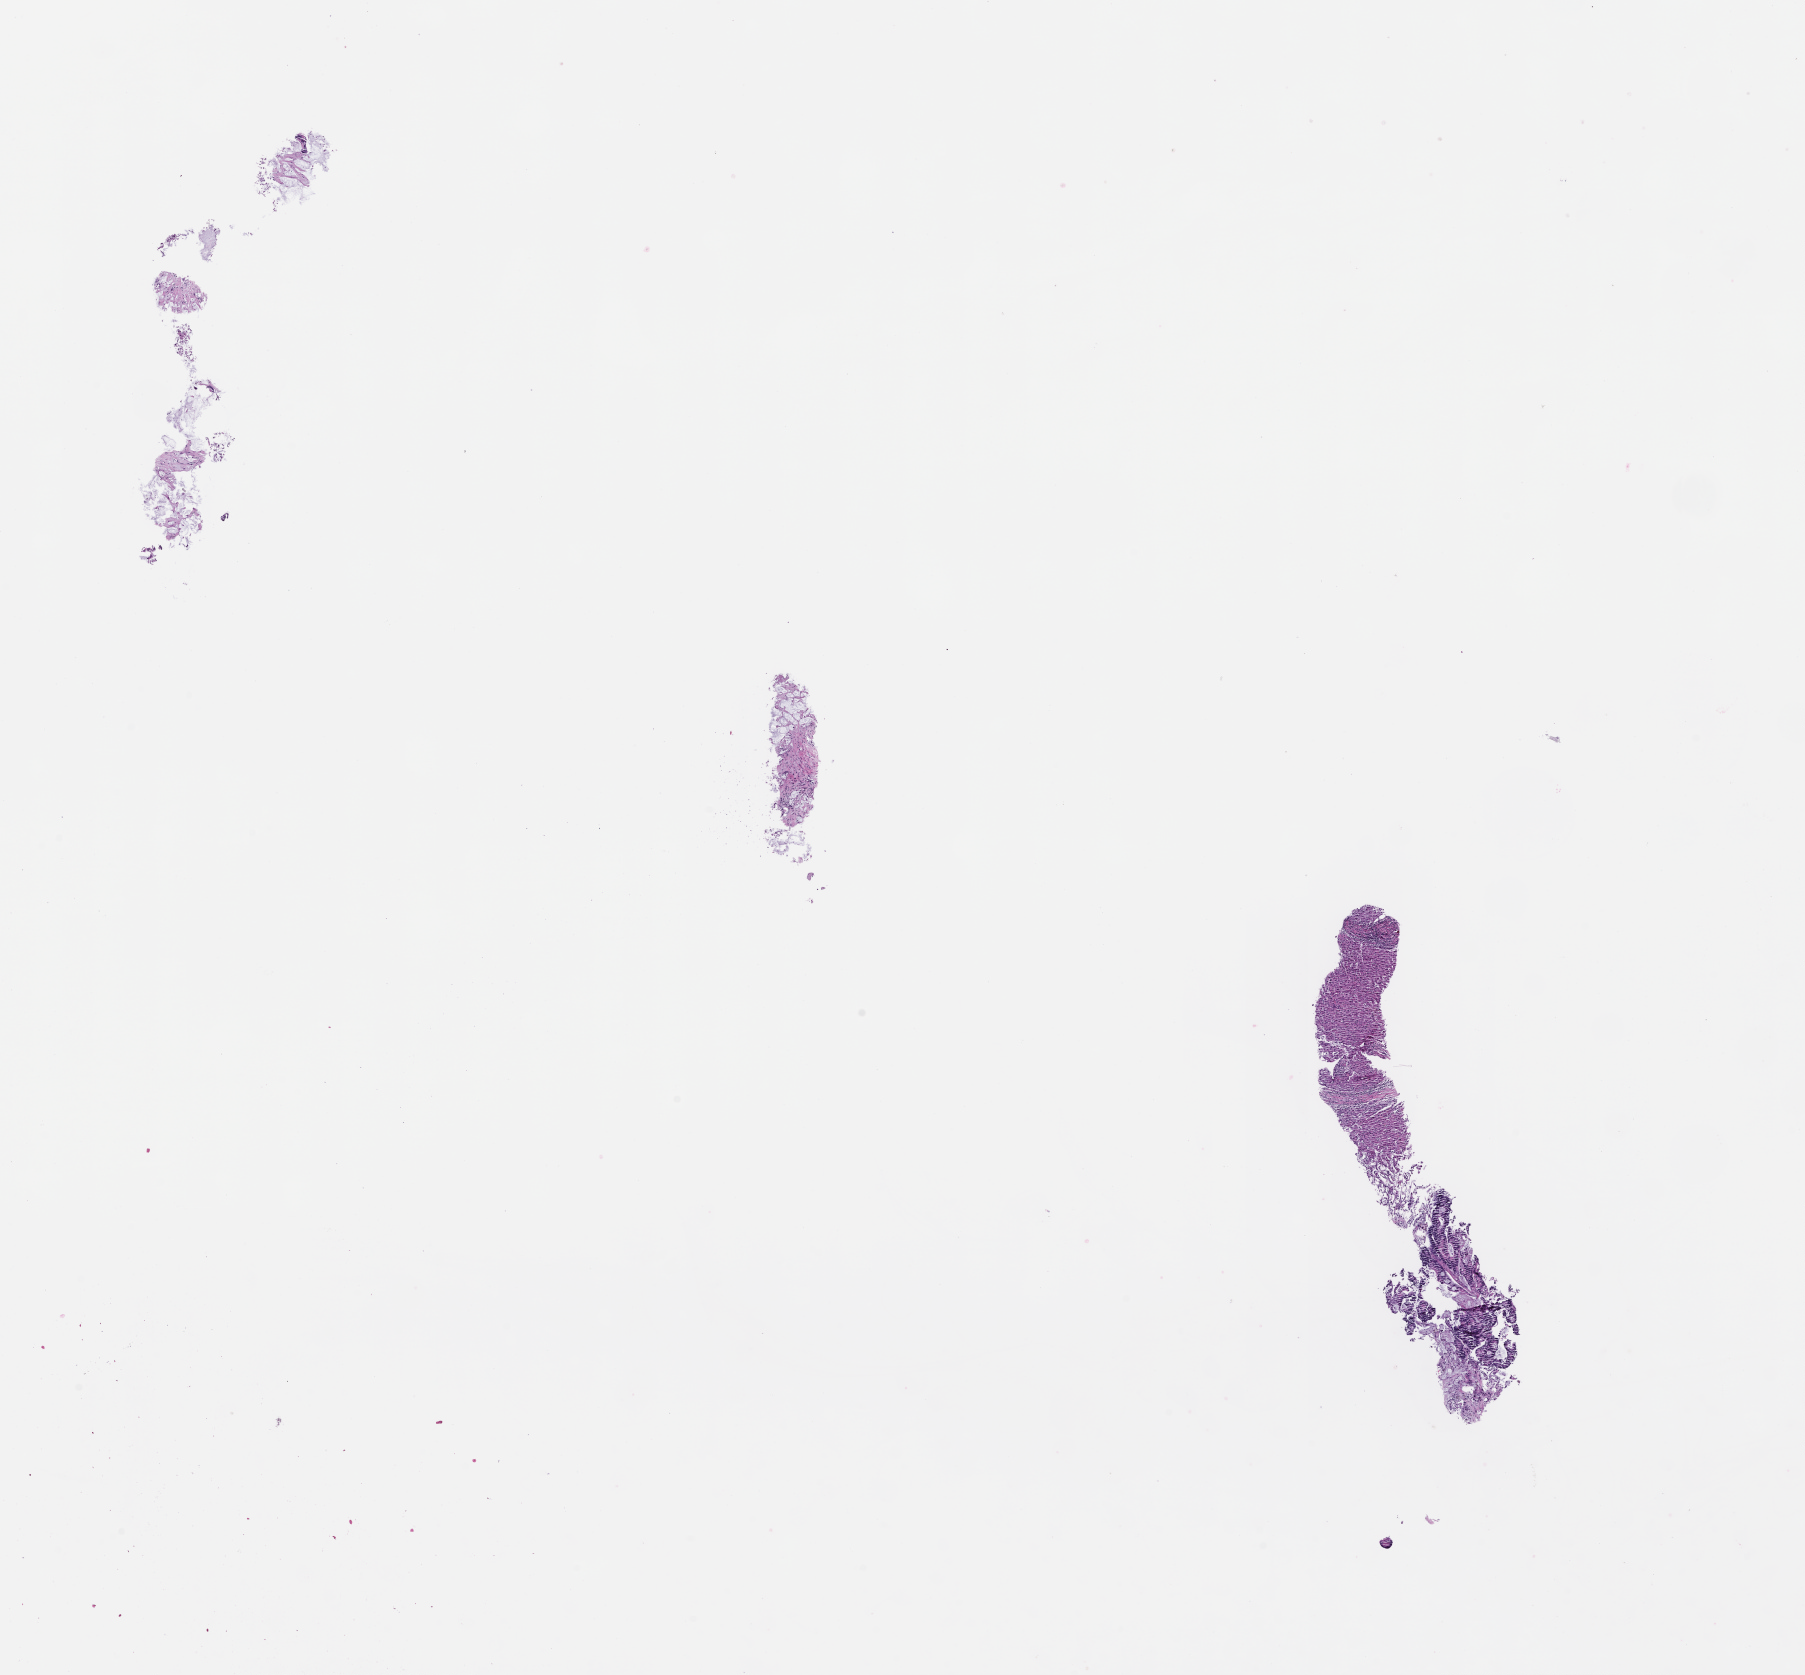
Digitized haematoxylin and eosin-stained section — shown as a low-resolution overview of the whole scanned area (about 14.6 x 13.5 mm). FFPE section. Specimen time point: collected at baseline (before treatment). Male patient.
This section: metastasis (sampled organ not recorded). Primary diagnosis of the patient: Colorectal Carcinoma.